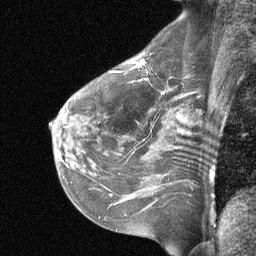
Breast MRI (dynamic contrast-enhanced), one sagittal slice. Position 40 of 64 along the scan axis. Dynamic contrast-enhanced study with each time point stored as its own series, time point 2 of 3 at this slice position (early post-contrast, ordered by acquisition time). 1.5 T. TE 4.8 ms, TR 27 ms. 256 × 256 image matrix, field of view 200 × 200 mm. Patient: female, 51 years. Case-level facts recorded for this patient, not image findings: setting: breast cancer imaged before/during neoadjuvant chemotherapy; receptor status: HR-positive, HER2-negative.
Outlined on this slice (semi-automatic segmentation, software-assisted and operator-edited):
- analysis volume of interest (the breast-tissue region the enhancement analysis was run in; not a lesion): bounding box <88,42,196,119> (left, top, right, bottom; pixels)
- tumour enhancement mask (voxels above the 90 % enhancement threshold inside the analysis volume of interest): <134,60,145,68>